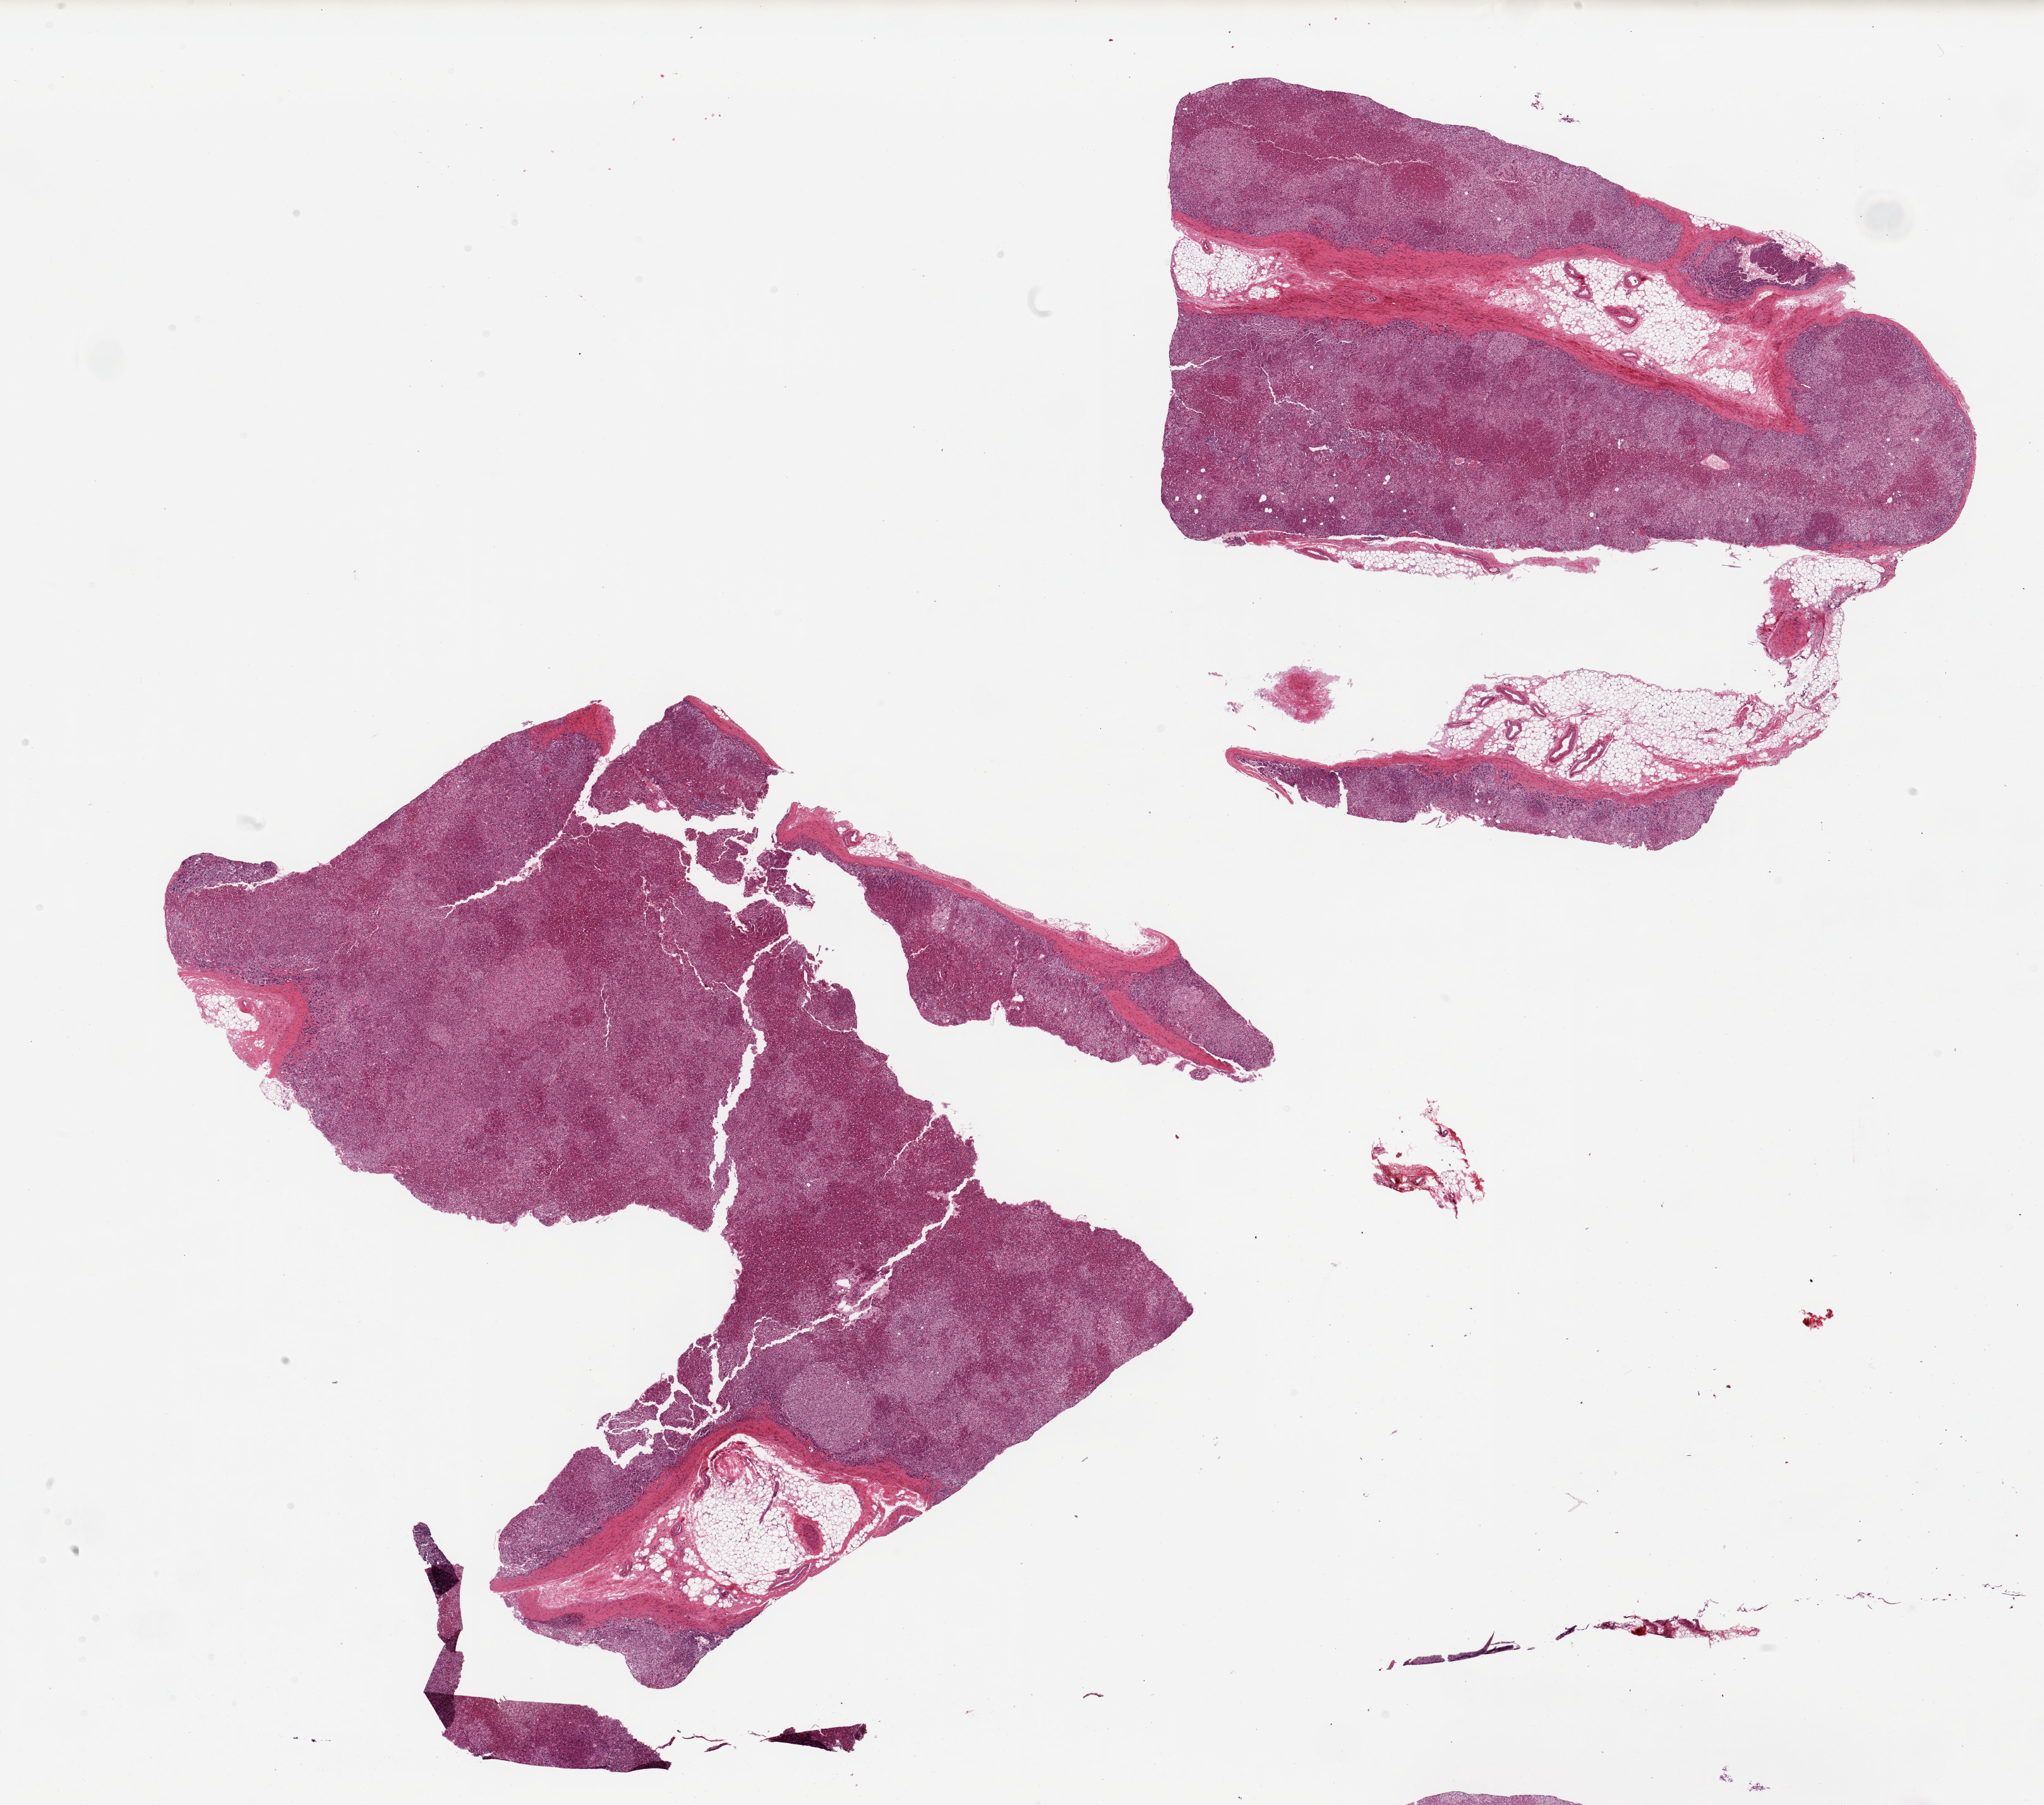
Haematoxylin and eosin whole-slide image, whole scanned area (about 25.6 x 22.6 mm, slide scanned at 20x) shown as a low-resolution overview; PAXgene-fixed paraffin-embedded (PFPE) section; sampled site (target tissue): adrenal gland; donor tissue sample. Donor sex: female.
* pathologist's review note for this sample: 2 pieces, all cortex, well preserved, ~10% adherent / interstitial fate